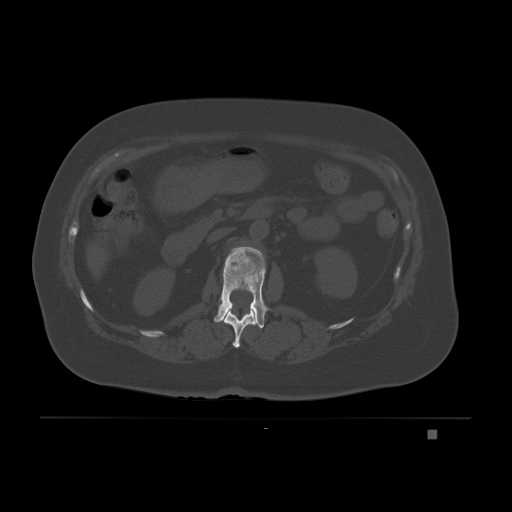
CT including the spine, one axial slice. Position 73 of 221 along the scan axis. Bone window (W 1800 / L 400 HU). 3 mm slice thickness. 512 × 512 image matrix, field of view 474 × 474 mm. Patient: female, 63 years. Case-level facts recorded for this patient, not image findings: primary cancer: breast.
Structures marked on this image (semi-automatically segmented with operator editing):
- L1 vertebra: bounding box <214,246,270,328> (left, top, right, bottom; pixels)
- T12 vertebra: <224,309,257,348>